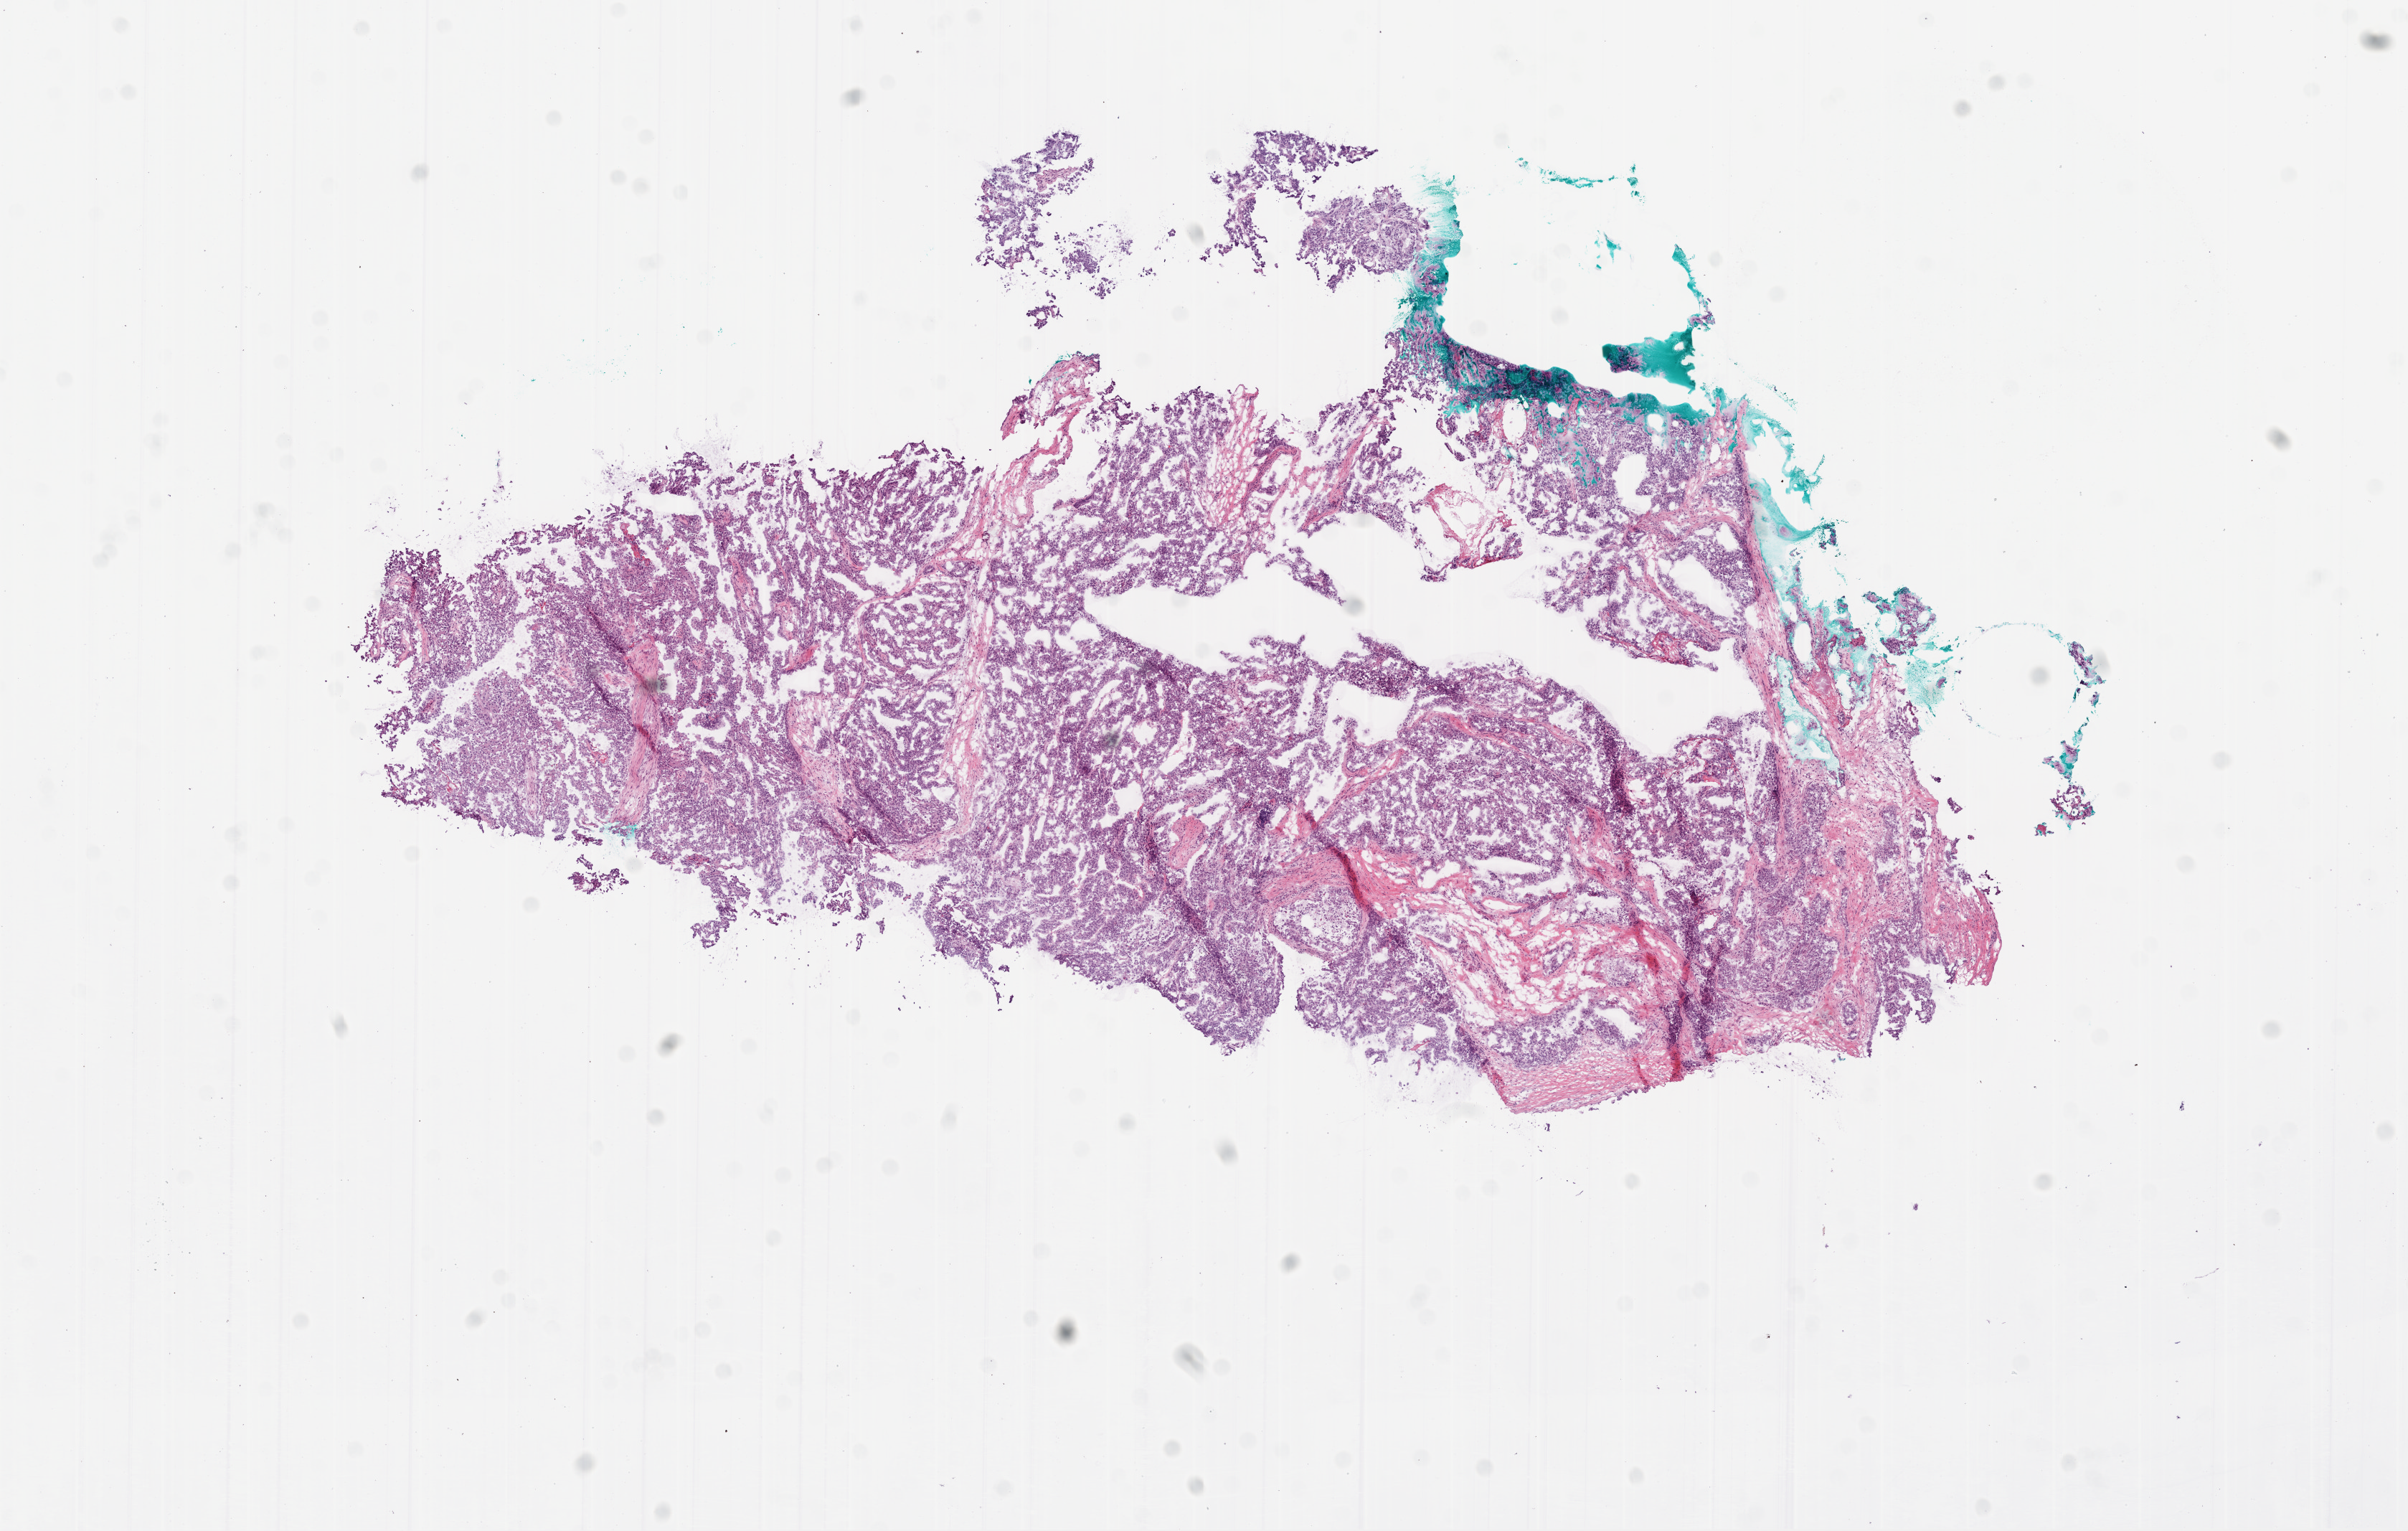
H&E whole-slide image, shown as a low-resolution overview of the whole scanned area (about 13.5 x 8.6 mm, slide scanned at 20x); frozen section; primary tumour sample from the ovary. Female, age 54 years at initial diagnosis. Histologic grade: G3 (poorly differentiated). Pathologist review of this section (percent, as recorded): tumour cells 80%, tumour nuclei 83%, normal cells 17%, necrosis 3%.
FIGO stage: IIIC. Diagnosis: Serous cystadenocarcinoma, NOS.